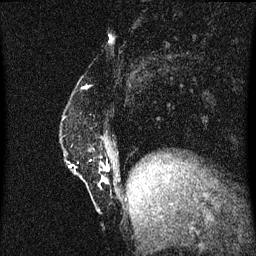
Breast MRI (dynamic contrast-enhanced), one sagittal slice; position 11 of 60 along the scan axis; dynamic contrast-enhanced series, image 2 of 3 at this slice position (ordered by acquisition); 1.5 T; TE 4.2 ms, TR 8.4 ms; 2 mm slice thickness; 256 × 256 image matrix. Female patient, age 52 years. From the clinical record (not read from this slice): setting: breast cancer imaged before/during neoadjuvant chemotherapy; receptor status: HER2-positive.
Annotated regions visible in this slice (semi-automatically segmented with operator editing):
- analysis volume of interest (the breast-tissue region the enhancement analysis was run in; not a lesion): box from (x=70, y=138) to (x=117, y=183) px
- tumour enhancement mask (voxels above the 70 % enhancement threshold inside the analysis volume of interest): (x=103, y=170)–(x=108, y=183)